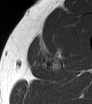
MRI of an extremity soft-tissue mass, one axial slice. Position 46 of 62 along the scan axis. MR volume resampled by the dataset authors to the PET/CT grid (not the native acquisition matrix). 3.27 mm slice thickness. 92 × 104 image matrix. Male patient. From the clinical record (not read from this slice): histological type: mixoid liposarcoma; grade: low; site of the primary tumour: left thigh.
Structures marked on this image (expert contour drawn on MRI and transferred to this co-registered scan by the dataset authors):
- gross tumour volume (mass): bounding box (x1, y1, x2, y2) in pixels: (44, 44, 61, 57)